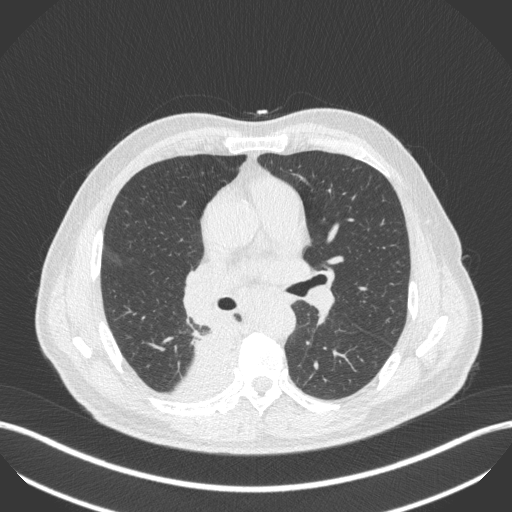
Chest CT, one axial slice. Position 265 of 451 along the scan axis. 100 kVp. Lung window (W 1500 / L -600 HU). 1 mm slice thickness. 512 × 512 image matrix, field of view 400 × 400 mm. Patient: male, 61 years. From the clinical record (not read from this slice): clinical TNM (as recorded): T1 N0 M0; histopathological grade: G3.
Outlined on this slice (rectangle marked by the reading radiologist):
- lung tumour (recorded histology: small cell carcinoma): bounding box <190,316,238,369> (left, top, right, bottom; pixels)